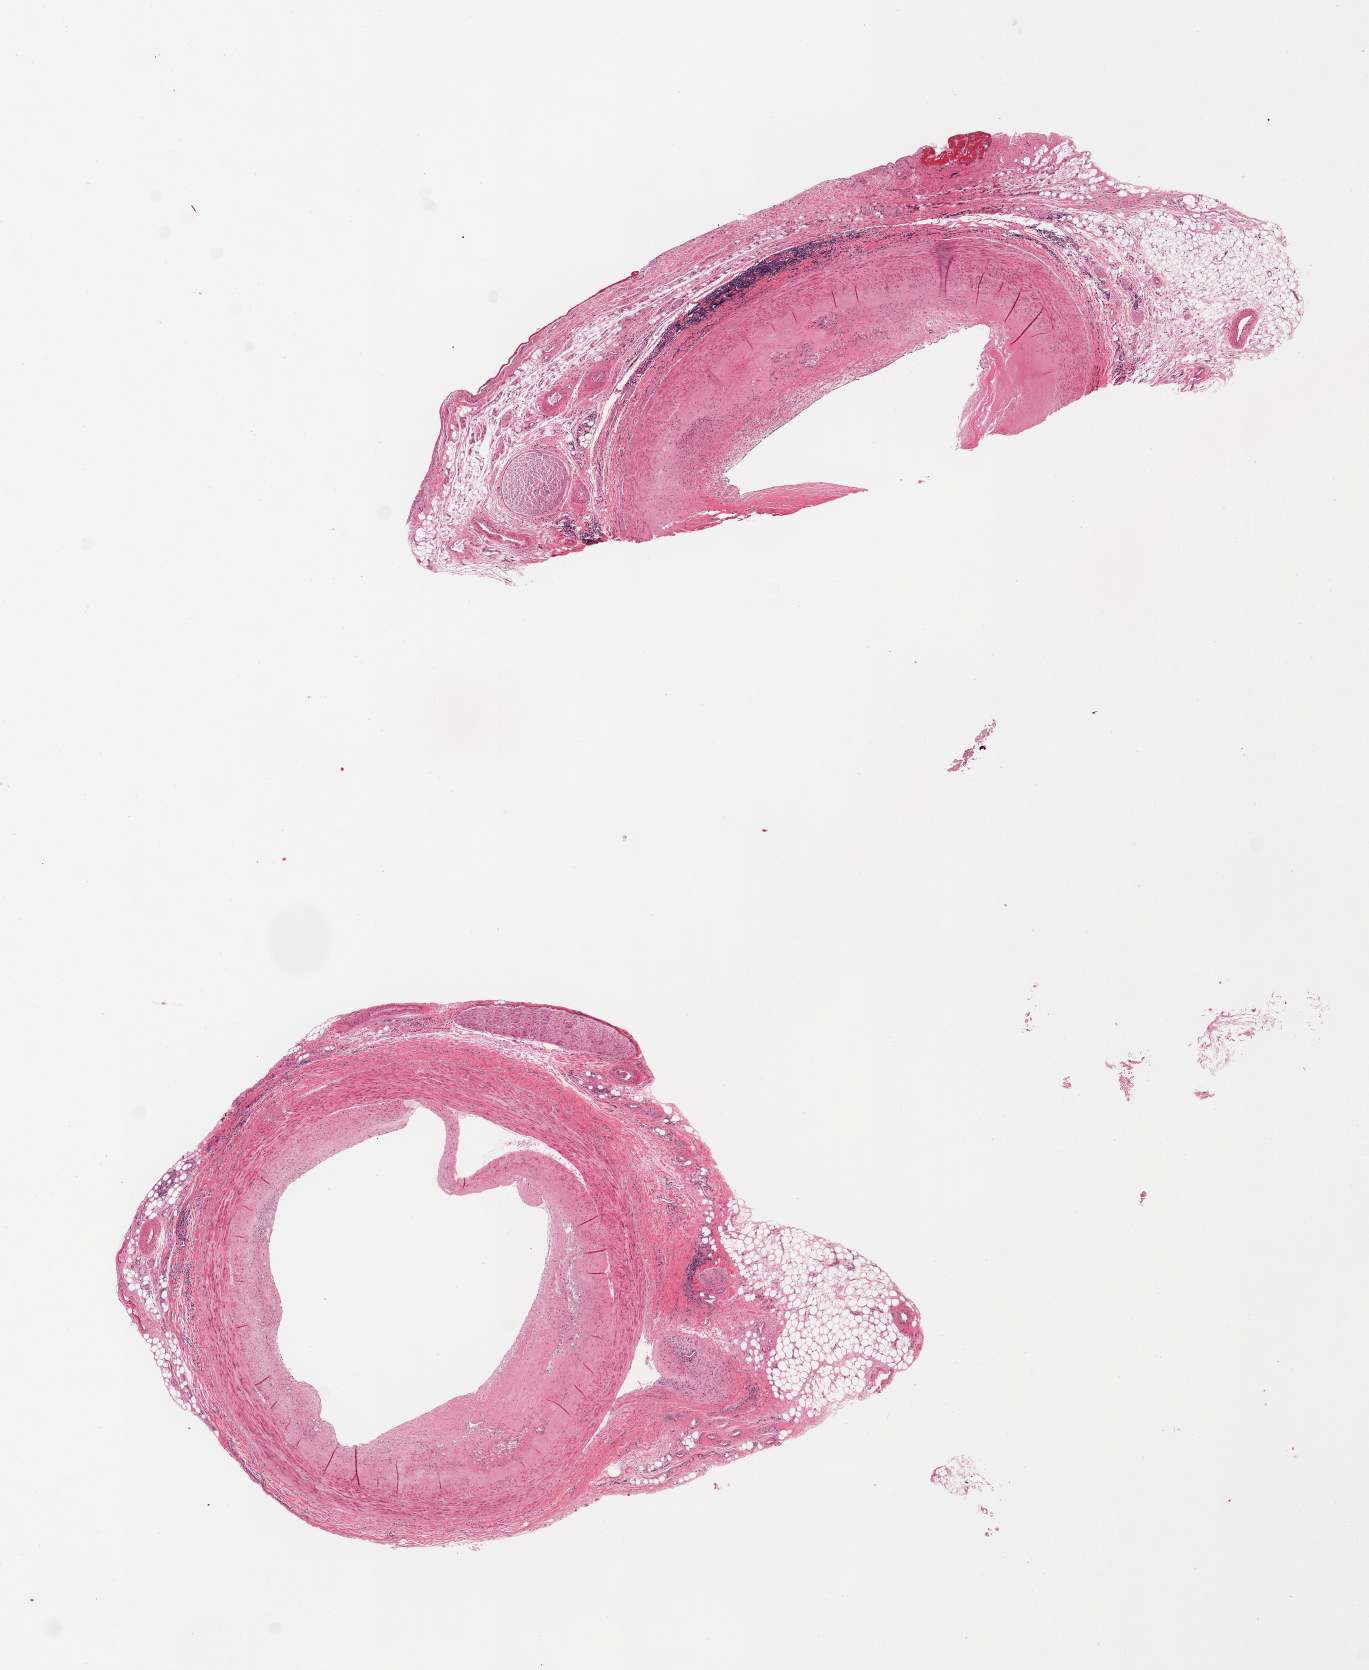
Digitized H&E-stained section — whole scanned area (about 10.8 x 13.2 mm) shown as a low-resolution overview. PAXgene-fixed paraffin-embedded (PFPE) section. Sampled site (target tissue): coronary artery. Tissue donor sample. Donor: male.
Pathologist's review note for this sample: 2 pieces, both with intimal plaques and perivascular fat up to 1.5 mm thick; focal adventitial lymphoid deposits [chronic inflammation].